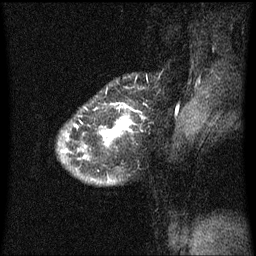
Breast MRI (dynamic contrast-enhanced), one sagittal slice; slice 53 of 60 in the series (ordered by position); dynamic contrast-enhanced series, image 2 of 3 at this slice position (ordered by acquisition); 1.5 T; TE 4.2 ms, TR 8.4 ms; 2 mm slice thickness; 256 × 256 image matrix, field of view 200 × 200 mm. Patient: female, 34 years. From the clinical record (not read from this slice): setting: breast cancer imaged before/during neoadjuvant chemotherapy; receptor status: HR-positive, HER2-negative.
Annotated regions visible in this slice (semi-automatic segmentation, software-assisted and operator-edited):
- analysis volume of interest (the breast-tissue region the enhancement analysis was run in; not a lesion): bounding box [x1, y1, x2, y2] px = [58, 88, 151, 187]
- tumour enhancement mask (voxels above the 70 % enhancement threshold inside the analysis volume of interest): [66, 120, 133, 153]